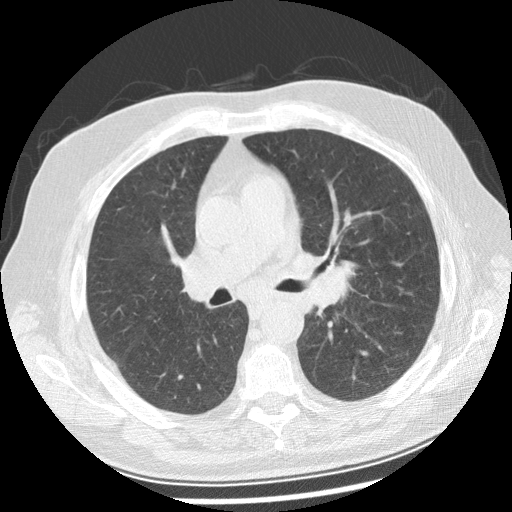
Low-dose screening chest CT, axial slice; first (baseline) screen; lung window (W 1500 / L -600 HU); 2.5 mm slice thickness; standard (soft-tissue) reconstruction kernel (STANDARD); 512 × 512 image matrix, field of view 360 × 360 mm. Male participant, aged 70 years at enrolment. Current smoker at enrolment.
Expert reader's lesion annotation, bounding box (x1, y1, x2, y2) in pixels: (282, 242, 364, 311). Screening reader's record for this exam: no non-calcified nodule ≥4 mm recorded. Official screen result: positive, change unspecified: nodule(s) >= 4 mm or enlarging nodule(s), mass(es), or other non-specific abnormalities suspicious for lung cancer. Participant outcome: lung cancer diagnosed 29 days after this screen — squamous cell carcinoma, keratinizing, NOS, left main stem bronchus, moderately differentiated (G2), stage IIIB (AJCC 6th edition), 40 mm at pathology.